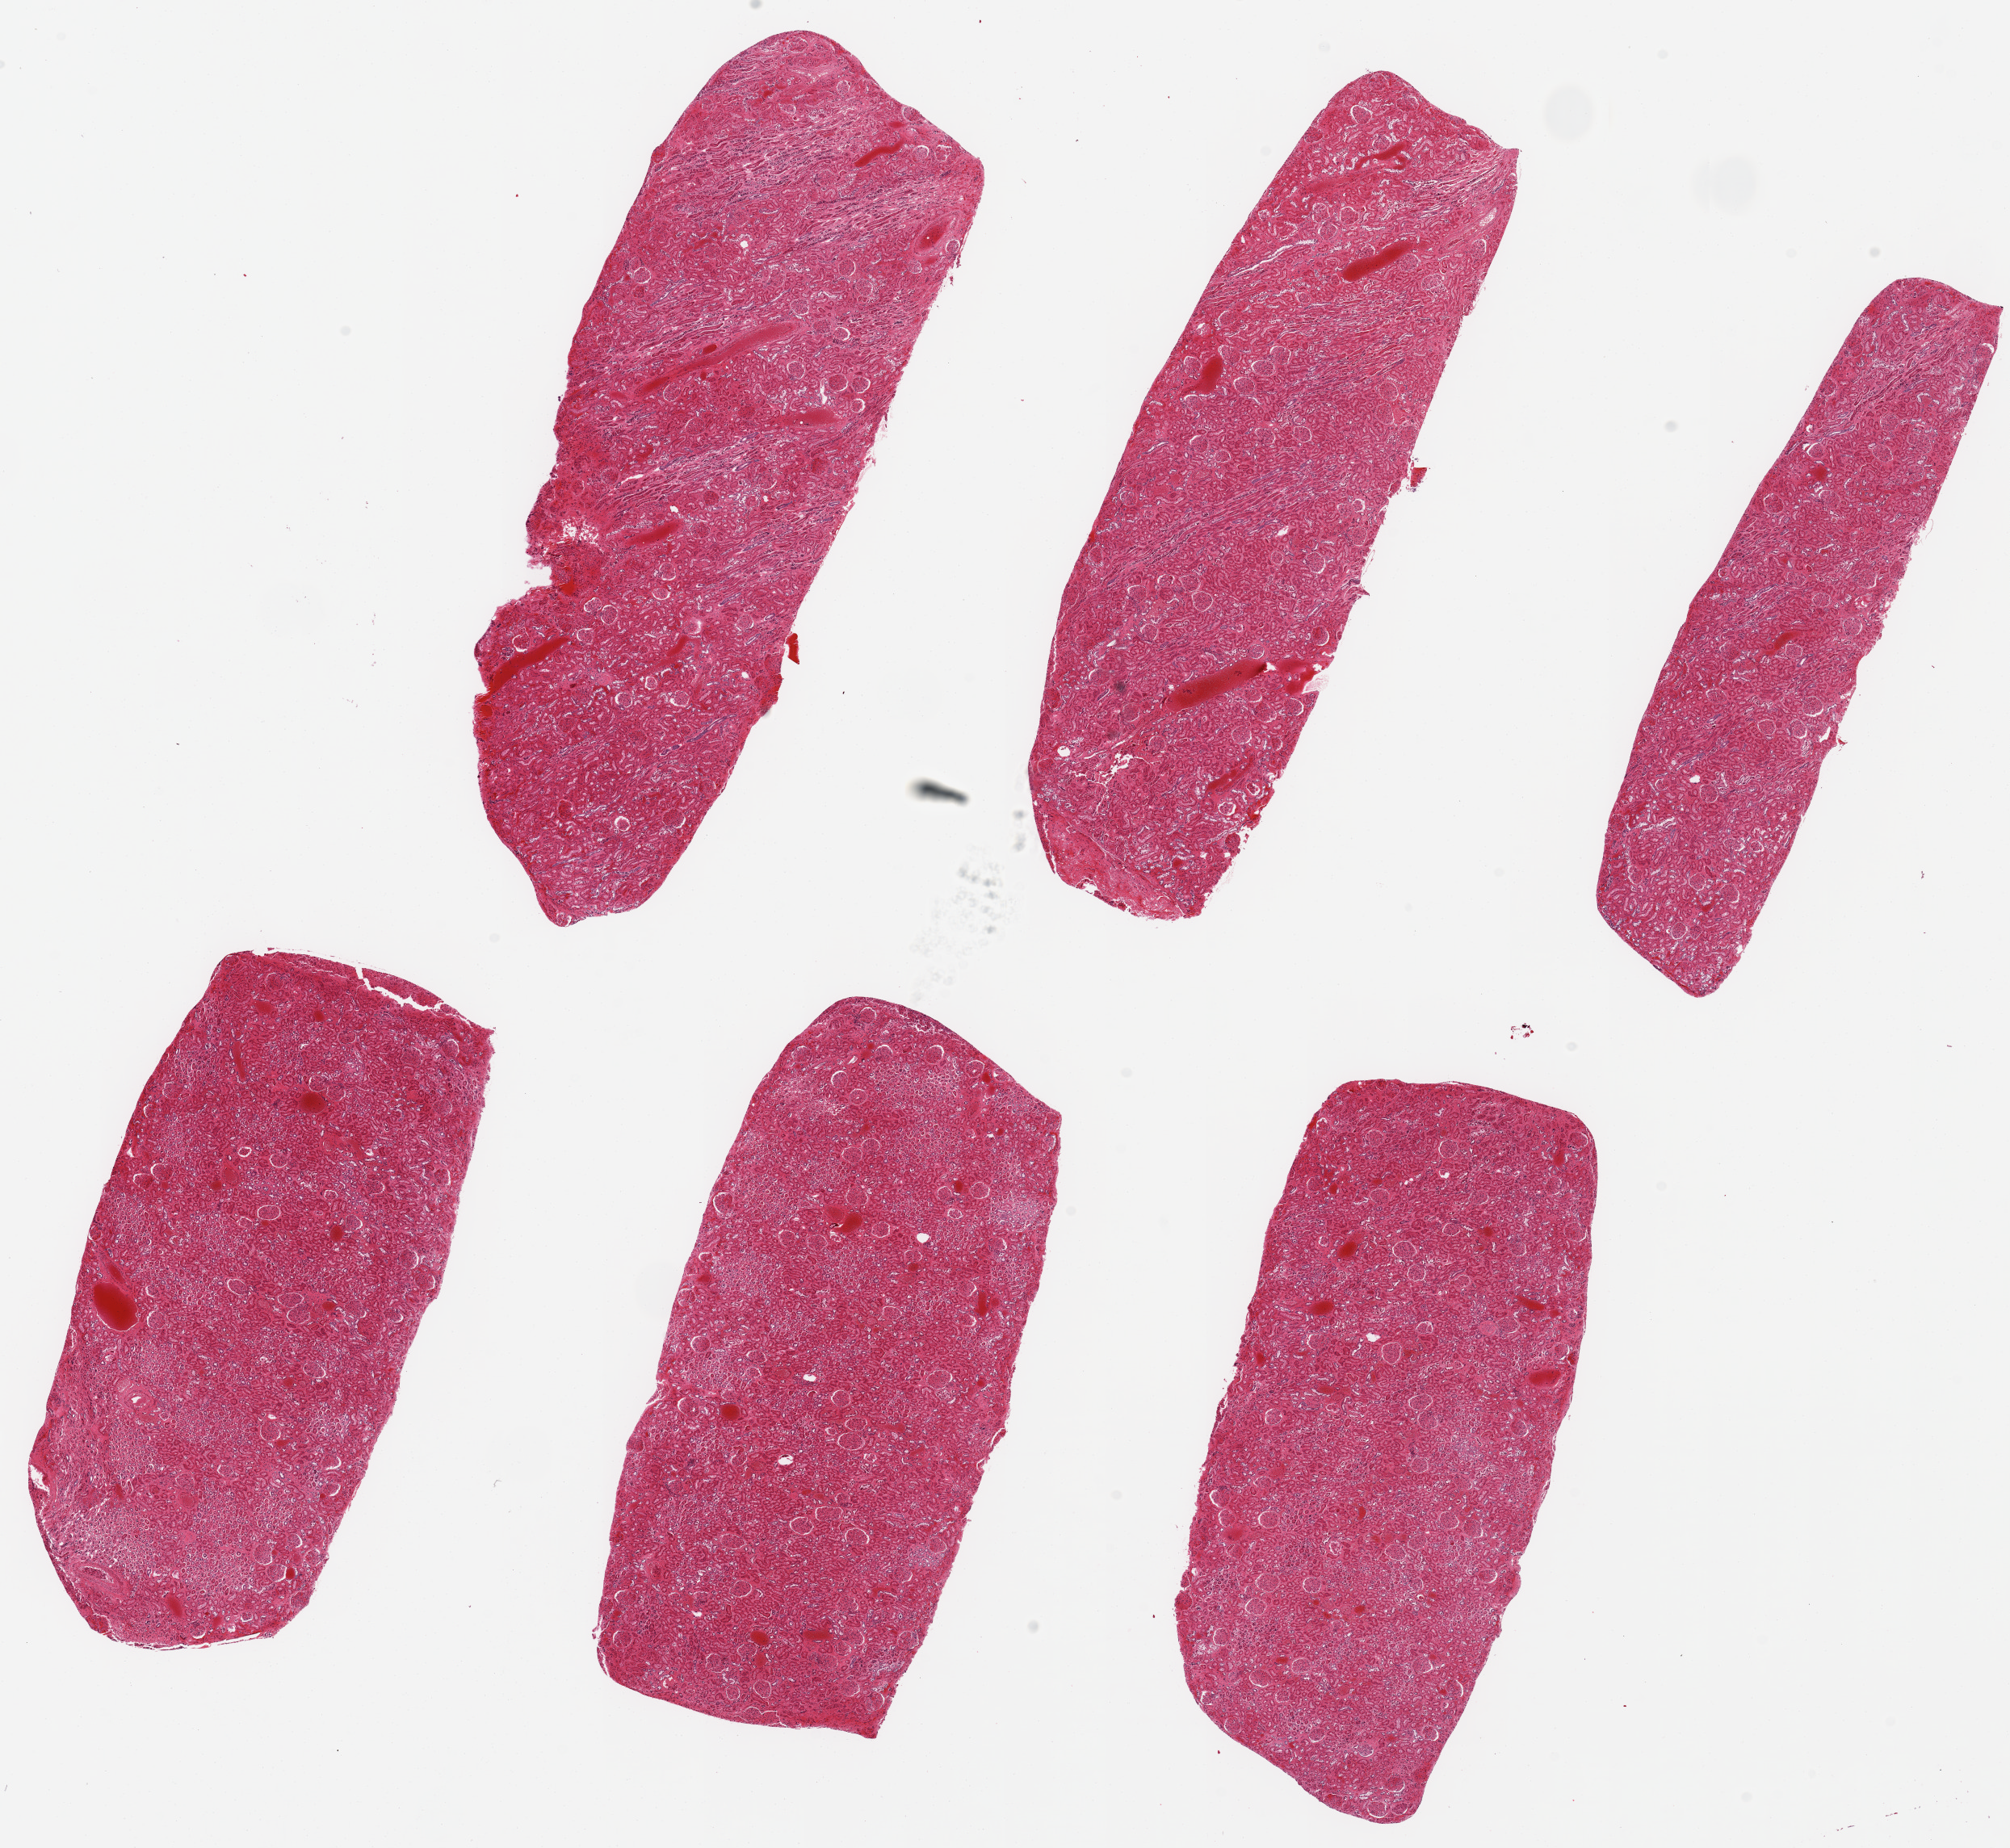
Digitized H&E-stained section — shown as a low-resolution overview of the whole scanned area (about 19.7 x 18.1 mm, slide scanned at 20x). PAXgene-fixed paraffin-embedded (PFPE) section. Sampled site (target tissue): renal cortex. Donor tissue sample. Donor: male.
Pathologist's review note for this sample: 6 ~7x3mm pieces. Marked diffuse congestion; abundant glomeruli. Tubules focally are badly autolyzed.